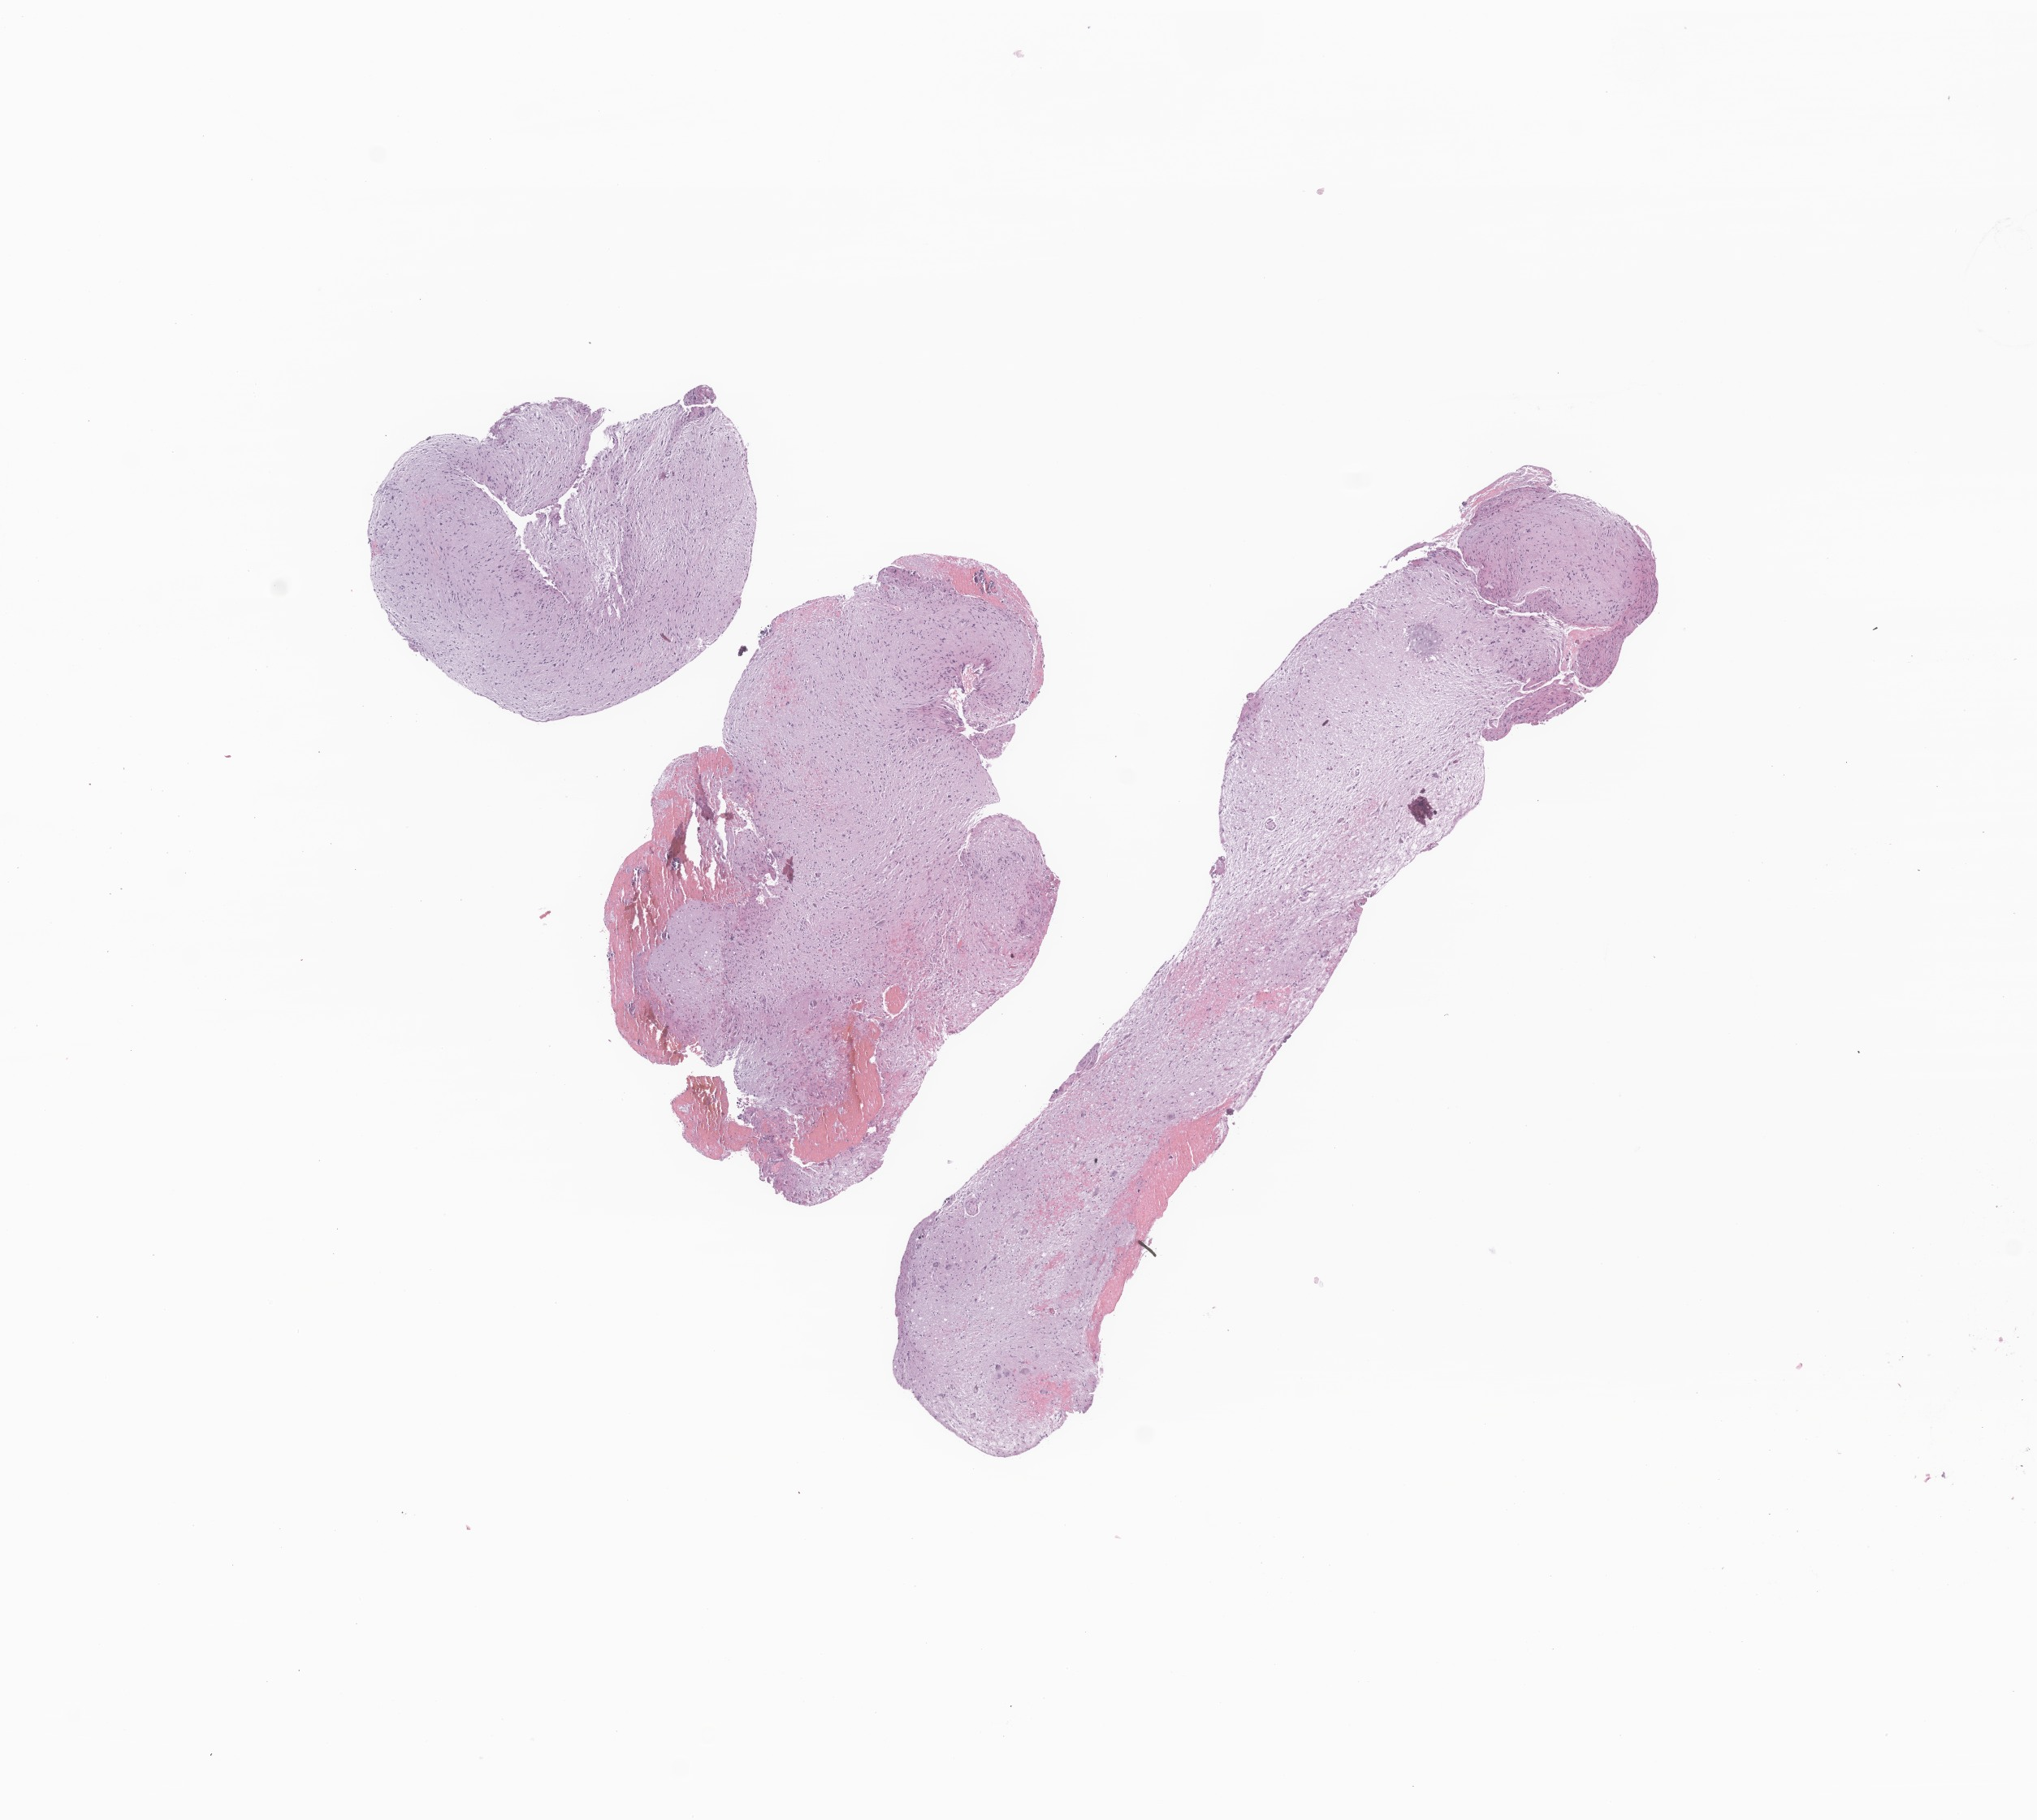
Digitized hematoxylin and eosin (H&E)-stained section of tumor tissue from the brain stem — shown as a low-resolution overview of the whole scanned area (about 10.6 x 9.5 mm). Formalin-fixed paraffin-embedded section. Male patient, age 236 months (19 years 8 months).
Diagnosis: Pilocytic astrocytoma.